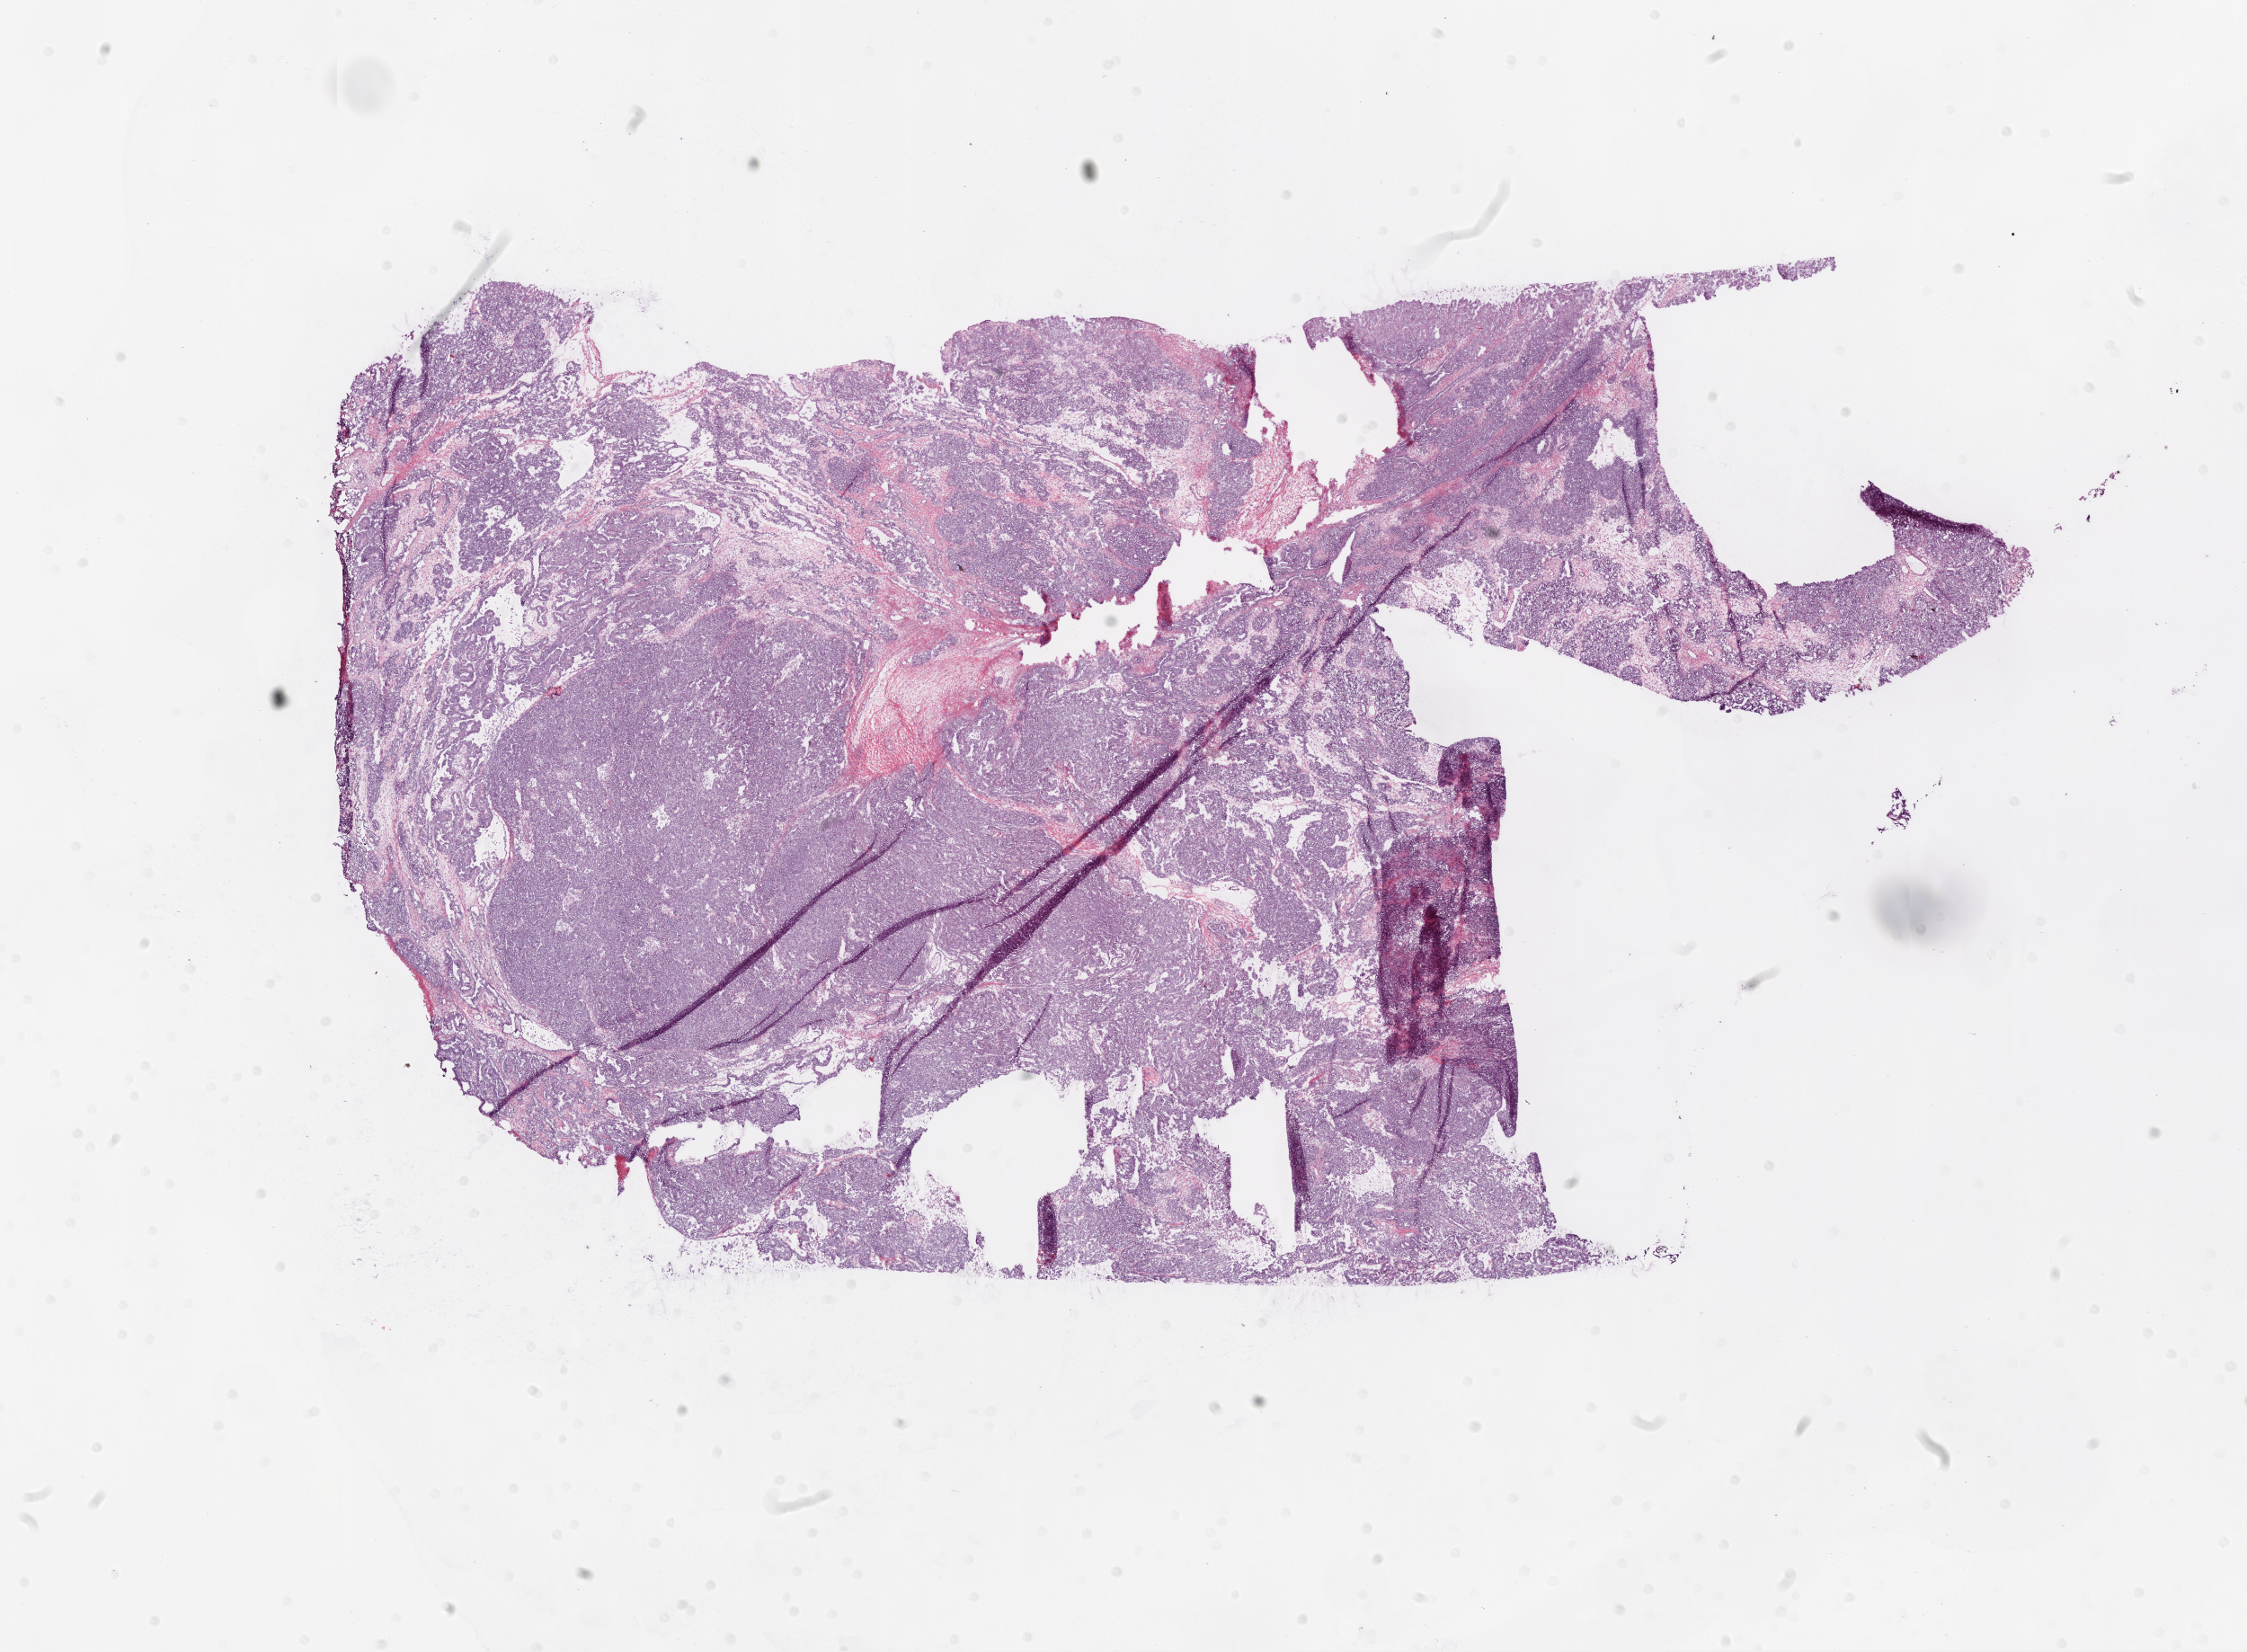
Whole-slide histology image, H&E-stained, a low-resolution overview of the entire scanned area, about 20.1 x 14.7 mm (acquisition: 20x scan); frozen section from the bottom of the tissue portion; primary tumour sample from the ovary. Female patient; age at initial diagnosis 50 years. Histologic grade: G2 (moderately differentiated). Slide review estimates, as recorded: tumour cells 94%, tumour nuclei 95%, normal cells 0%, stromal cells 5%, necrosis 1%.
• laterality: bilateral
• histologic diagnosis: Serous cystadenocarcinoma, NOS
• FIGO stage: IV